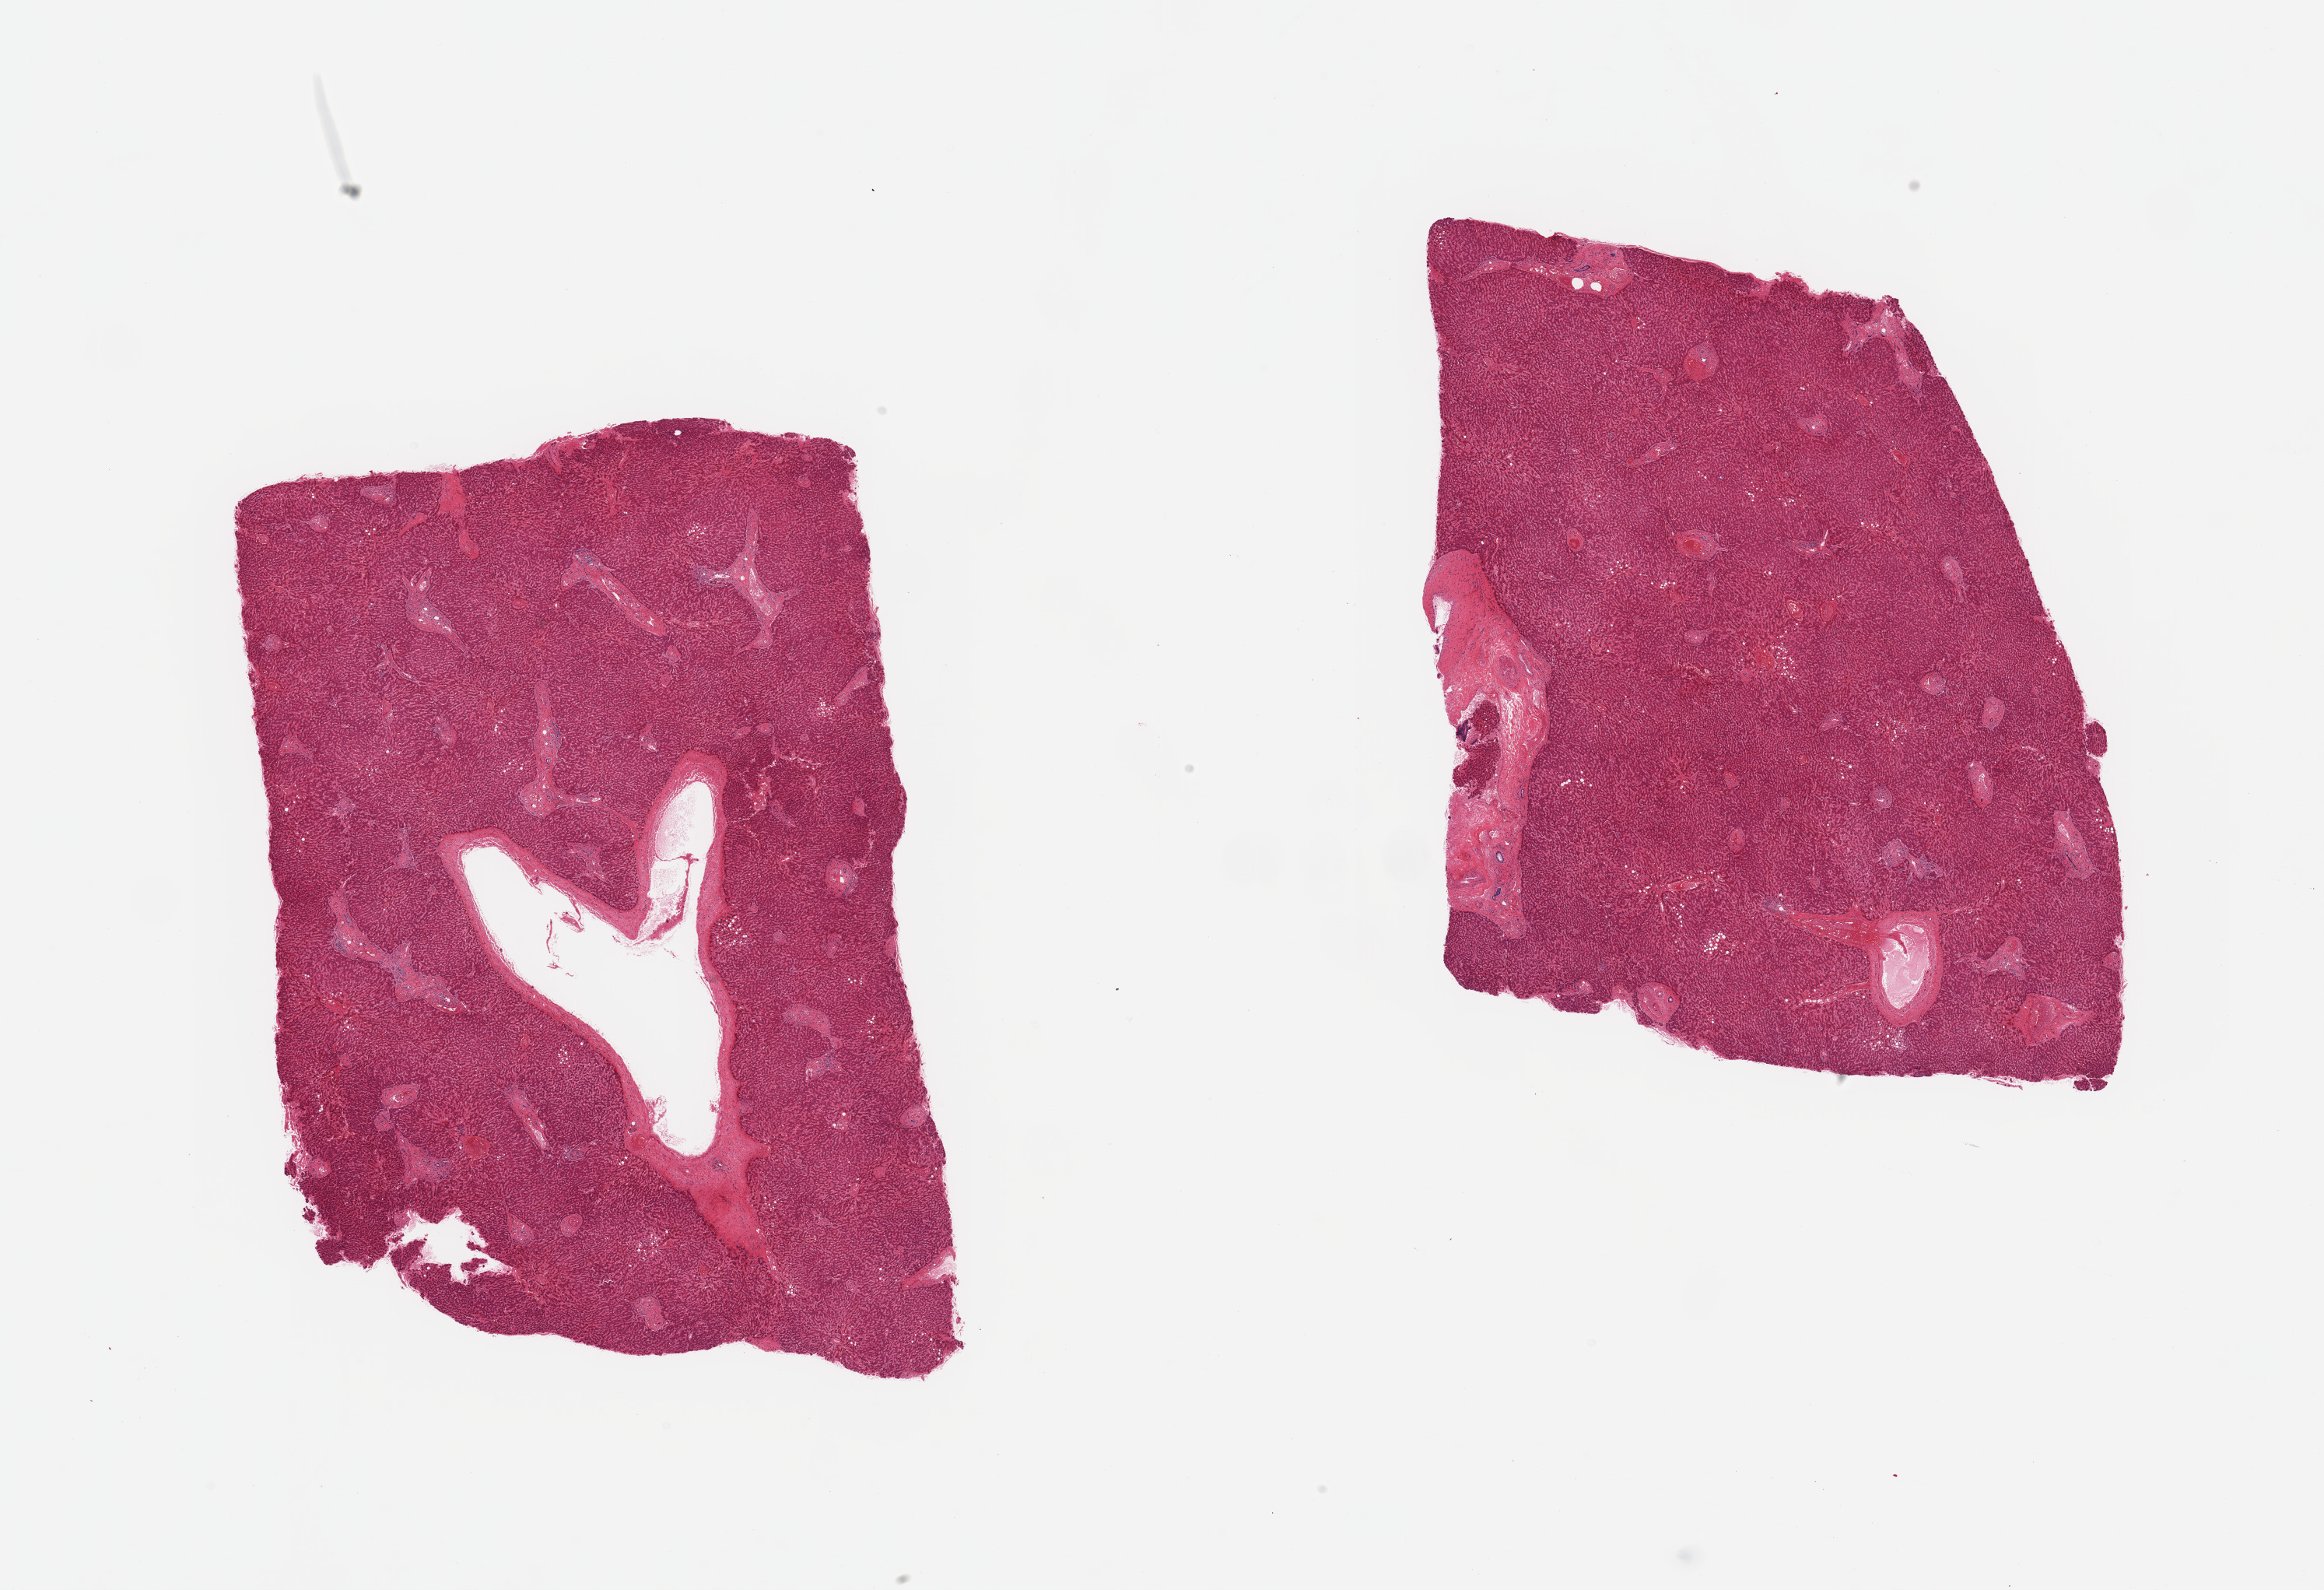
Whole-slide image, haematoxylin and eosin stain, brightfield, shown as a low-resolution overview of the whole scanned area (about 23.6 x 16.2 mm, slide scanned at 20x), PAXgene-fixed paraffin-embedded (PFPE) section, section of liver (target tissue), tissue donor sample. Male donor.
Pathologist's review note for this sample: 2 pieces; large [4 mm] vein in 1 piece; 4 x 0.7 mm fibrous area in other piece.